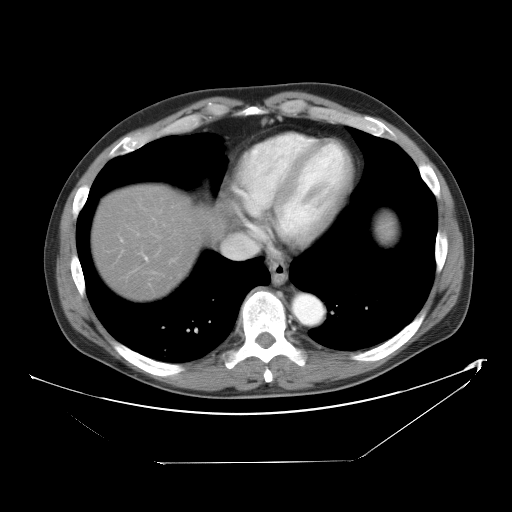
Contrast-enhanced abdominal CT, one axial slice. Slice 48 of 53 in the series (ordered by position). Reconstruction kernel STANDARD. 120 kVp. Intravenous contrast given. Soft-tissue window (W 400 / L 40 HU). 512 × 512 image matrix, field of view 438 × 438 mm. Male patient, age 59 years. From the clinical record (not read from this slice): diagnosis: colorectal cancer liver metastases, imaged before liver resection; multiple liver metastases: yes; largest metastasis: 8.5 cm; disease in both lobes: no.
Outlined on this slice (outlined manually by an expert reader):
- liver: box from (x=94, y=186) to (x=209, y=297) px
- planned liver remnant (the part of the liver to remain after resection): (x=94, y=189)–(x=201, y=298)
- portal vein (with intrahepatic branches): (x=145, y=257)–(x=148, y=261)